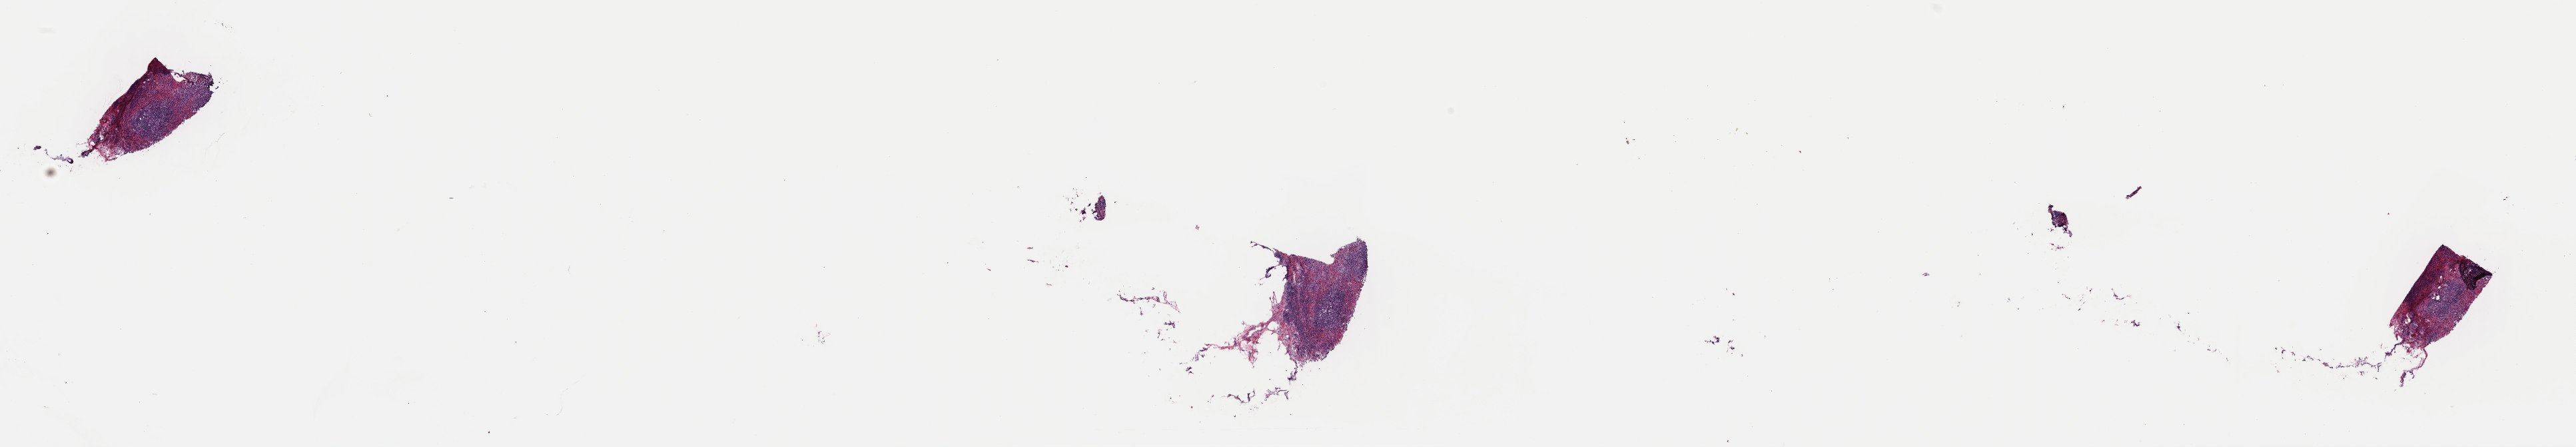
H&E whole-slide image — whole scanned area (about 30.5 x 5.3 mm) shown as a low-resolution overview. Frozen section. Metastatic tumour sample, sampled site not recorded. Female patient; age at initial diagnosis 49 years. Composition of this section per pathologist review: tumour cells 100%, tumour nuclei 75%, normal cells 0%, stromal cells 0%, necrosis 0%. Infiltration values recorded for this section: lymphocyte infiltration 5%, monocyte infiltration 0%, neutrophil infiltration 0%.
This section: metastatic tumour tissue. Patient diagnosis: Lobular carcinoma, NOS.